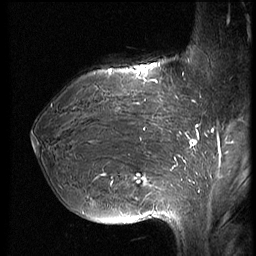
Breast MRI (dynamic contrast-enhanced), one sagittal slice. Slice 24 of 66 in the series (ordered by position). Dynamic contrast-enhanced series, image 2 of 3 at this slice position (ordered by acquisition). 1.5 T. TE 4.2 ms, TR 8.9 ms. 2.5 mm slice thickness. 256 × 256 image matrix. Female patient, age 39 years. Case-level facts recorded for this patient, not image findings: setting: breast cancer imaged before/during neoadjuvant chemotherapy; receptor status: HER2-positive.
Outlined on this slice (semi-automatically segmented with operator editing):
- analysis volume of interest (the breast-tissue region the enhancement analysis was run in; not a lesion): bounding box (x1, y1, x2, y2) in pixels: (32, 75, 188, 218)
- tumour enhancement mask (voxels above the 140 % enhancement threshold inside the analysis volume of interest): (100, 81, 183, 177)